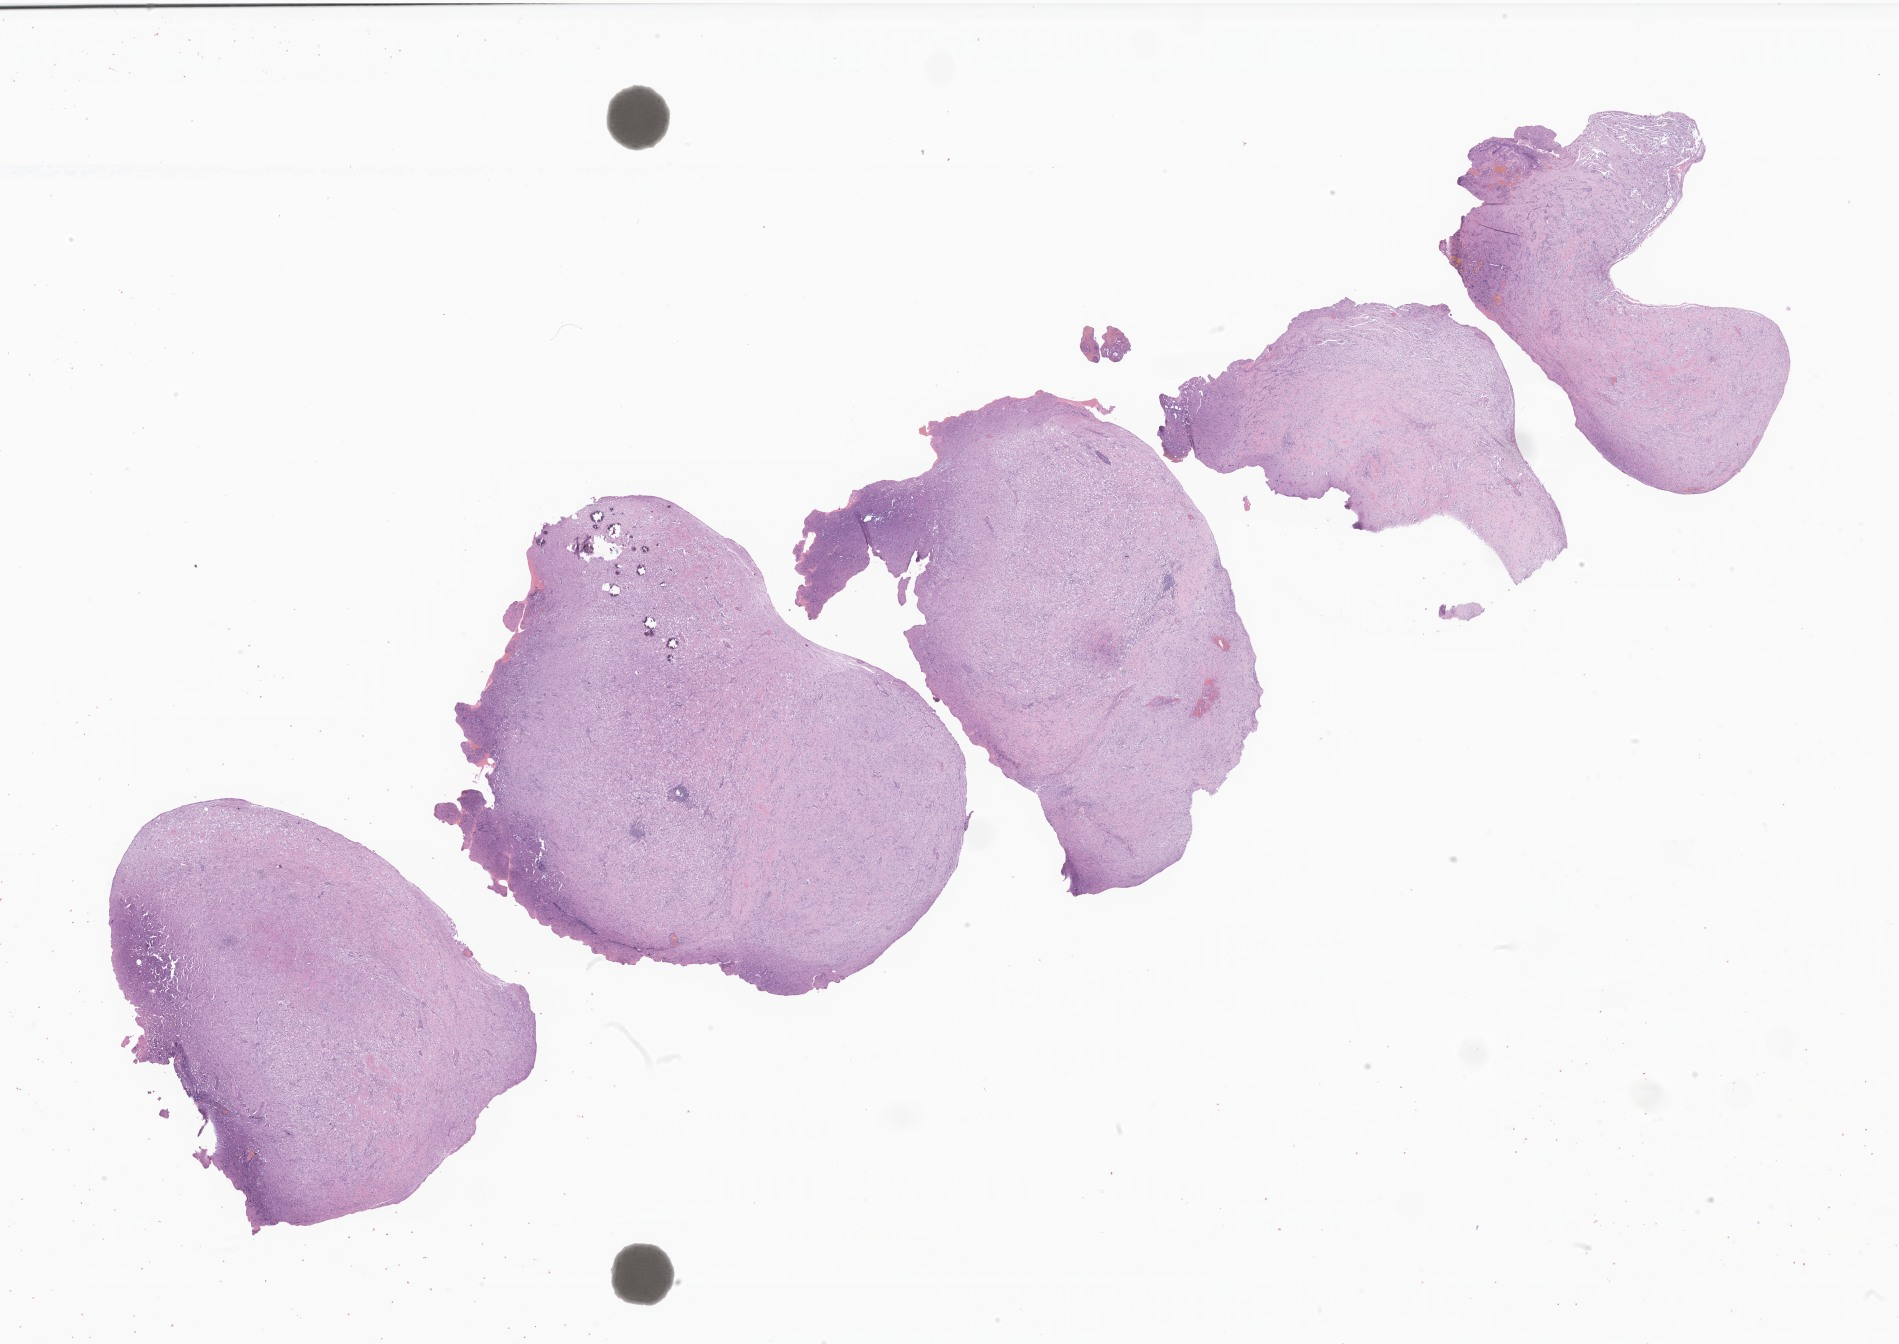
Whole-slide image, hematoxylin and eosin (H&E) stain of tumor tissue from the brain — whole scanned area (about 32.0 x 22.7 mm) shown as a low-resolution overview, formalin-fixed paraffin-embedded section. Female patient, age 189 months (15 years 9 months).
Diagnosis (ICD-O-3 morphology term): Tumor cells, uncertain whether benign or malignant.